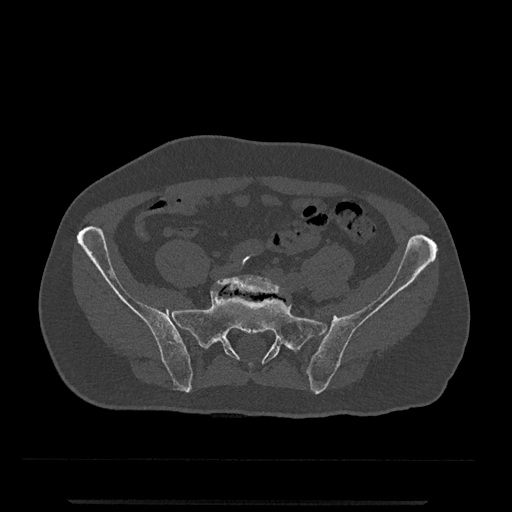
CT including the spine, one axial slice. Position 21 of 797 along the scan axis. Reconstruction kernel Br40s/3. 120 kVp. Bone window (W 1800 / L 400 HU). 0.5 mm slice thickness. 512 × 512 image matrix, field of view 419 × 419 mm. Male patient, age 63 years. Case-level facts recorded for this patient, not image findings: primary cancer: prostate.
Annotated regions visible in this slice (semi-automatically segmented with operator editing):
- L5 vertebra: bounding box [x1, y1, x2, y2] px = [215, 275, 283, 295]